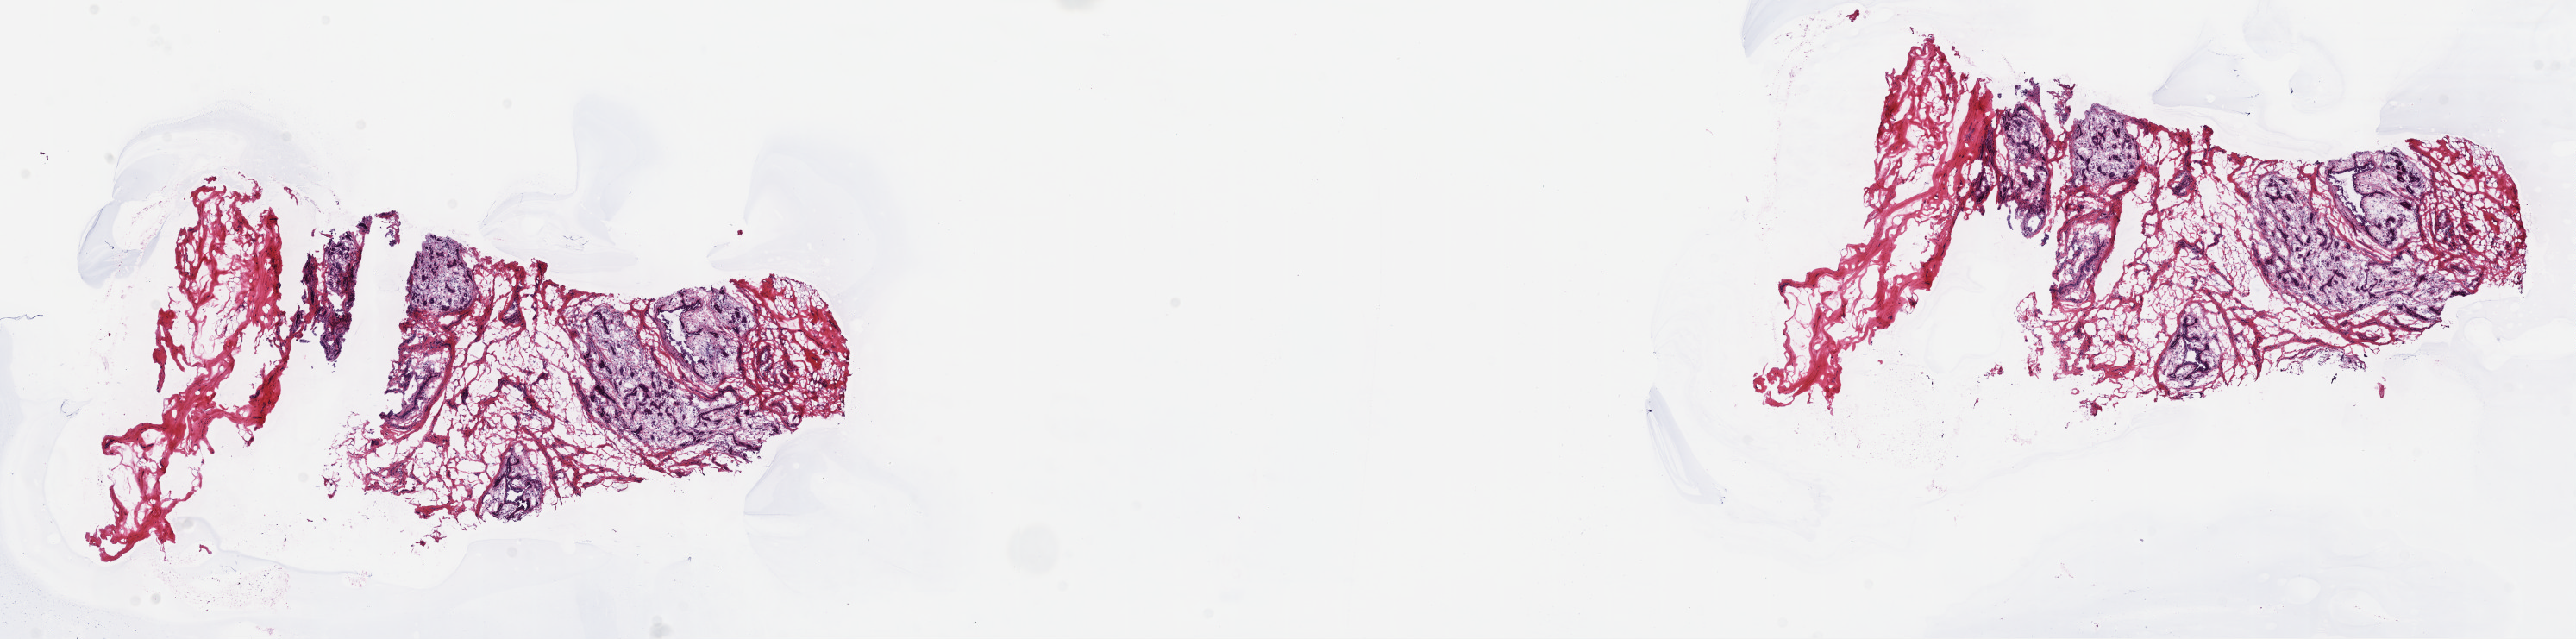
Whole-slide histology image, H&E-stained — shown as a low-resolution overview of the whole scanned area (about 24.2 x 6.0 mm, acquisition: 40x scan), formalin-fixed paraffin-embedded (FFPE) diagnostic section, primary tumour sample from the breast. Patient: female, age at initial diagnosis 30 years.
Laterality: right. AJCC pathologic stage: IIB. Histologic diagnosis: Infiltrating duct carcinoma, NOS.